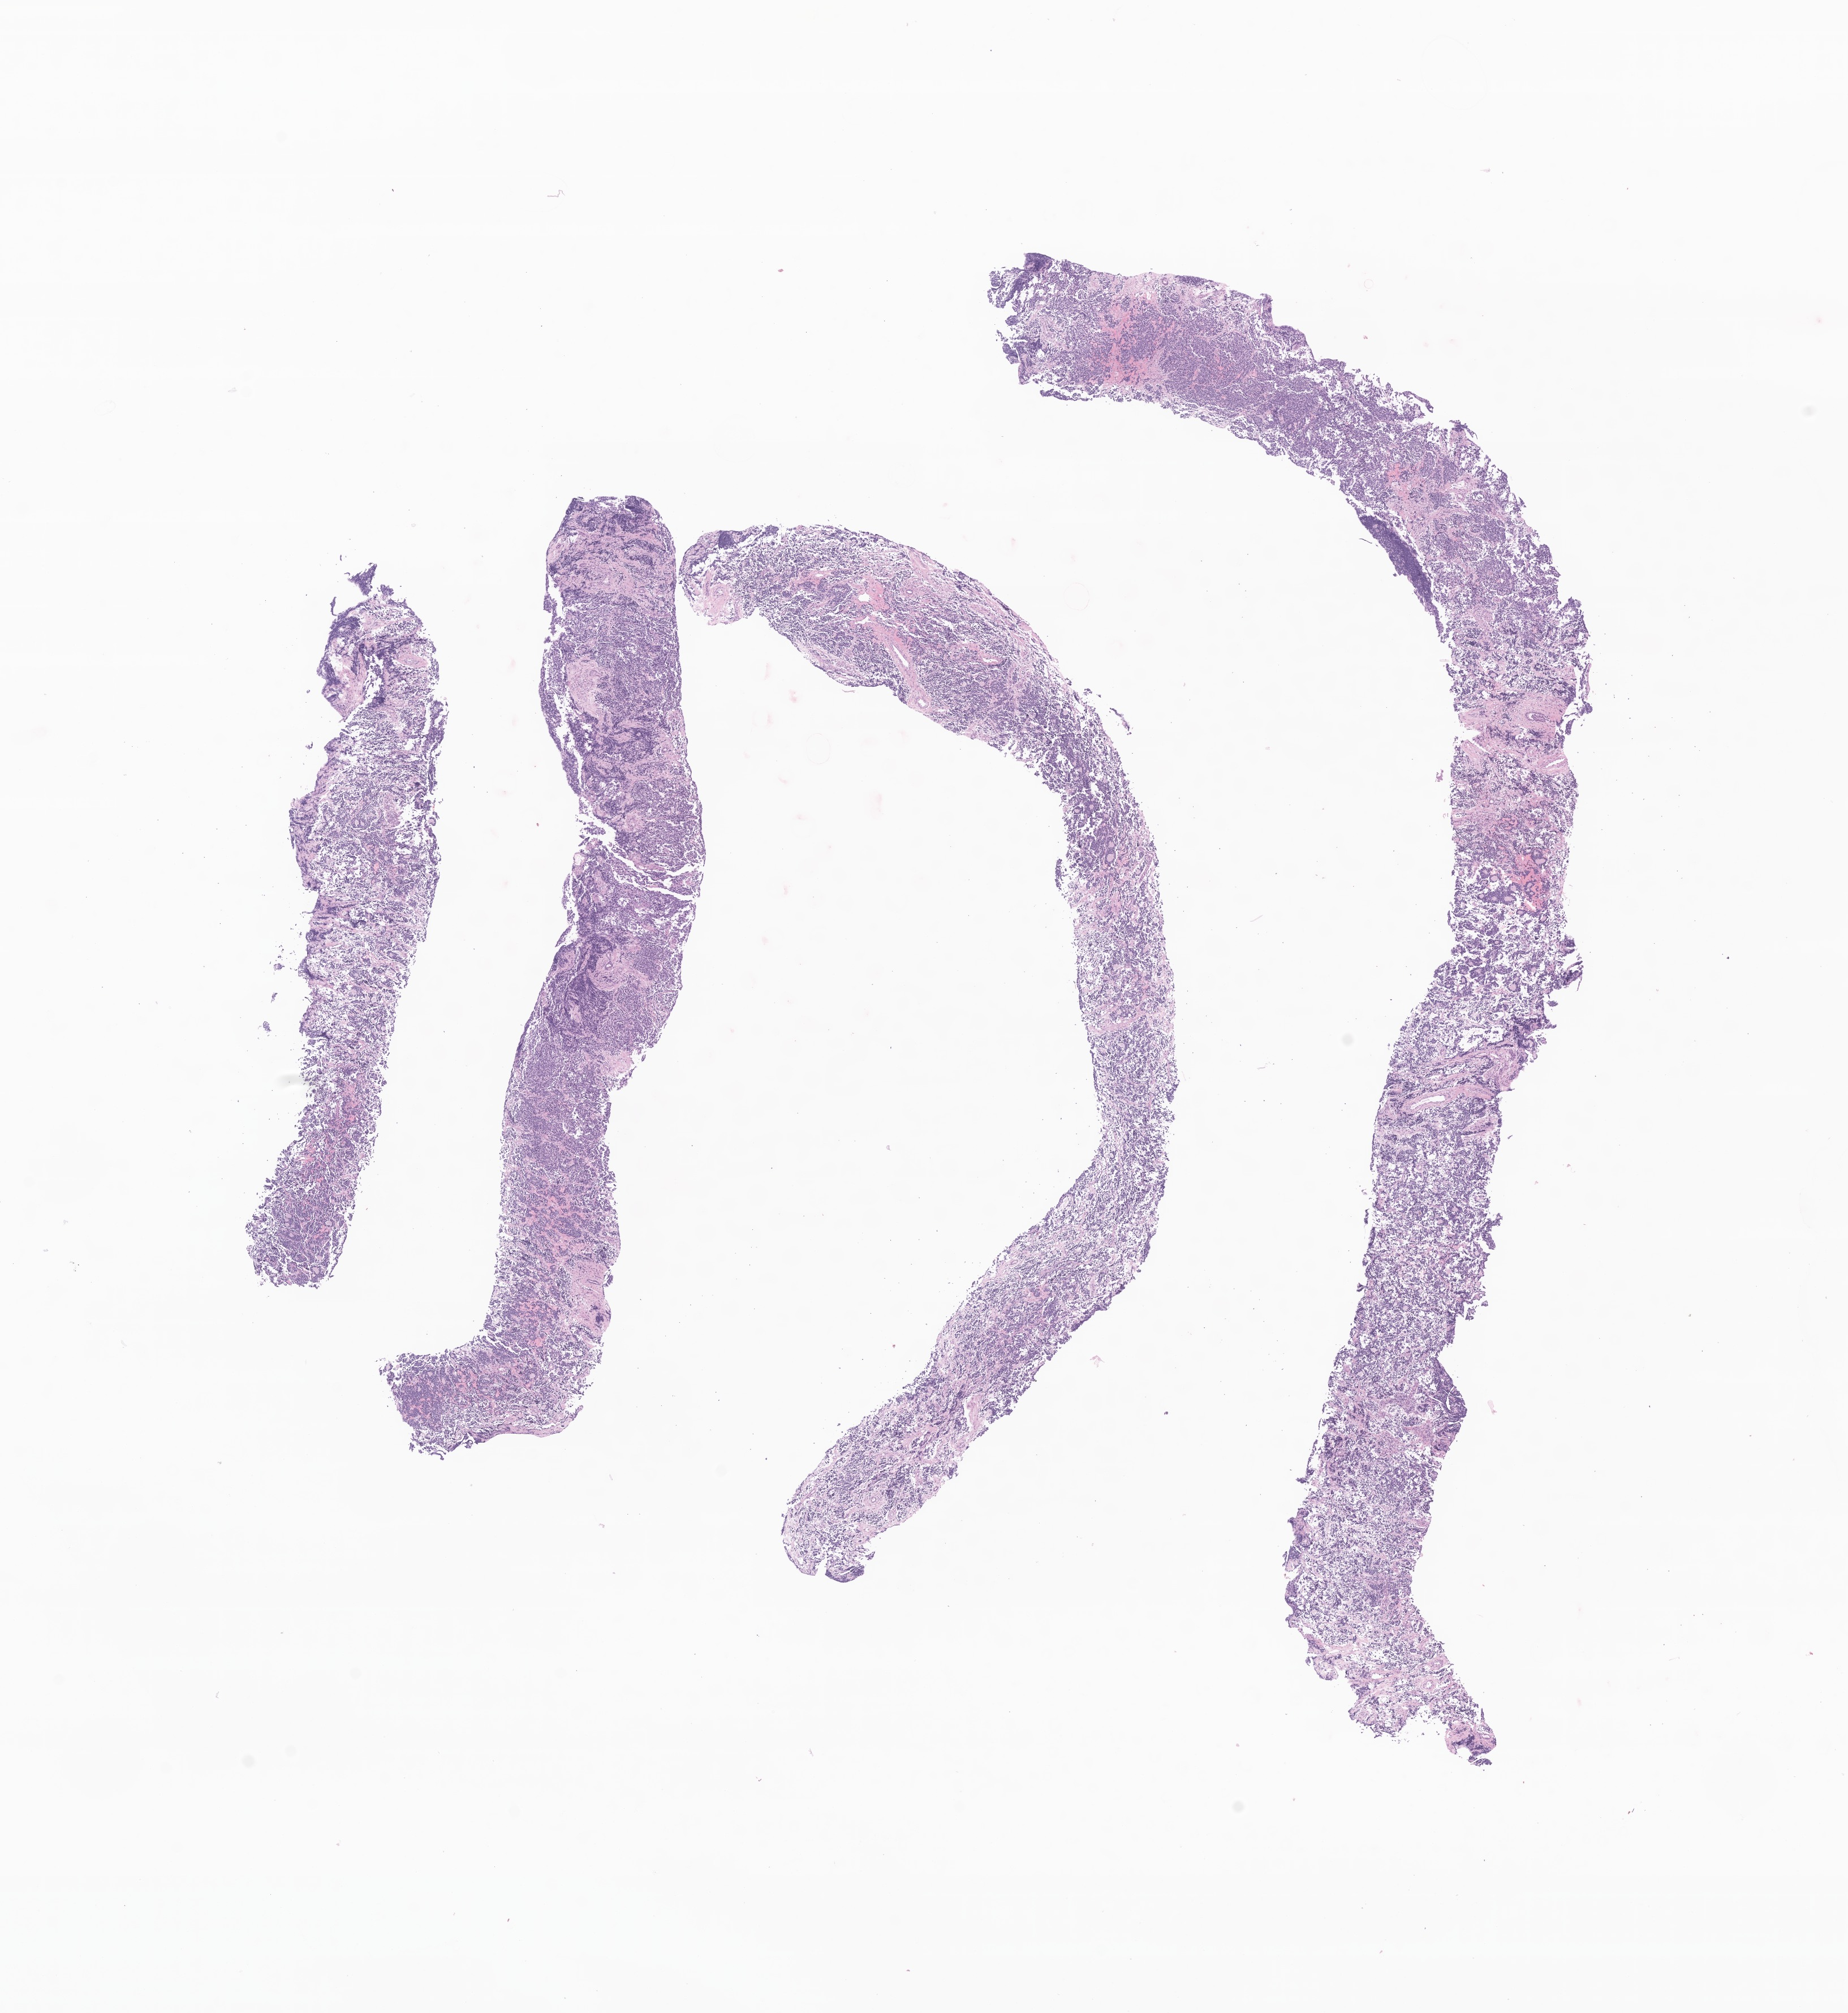
Whole-slide image, haematoxylin and eosin stain of tumor tissue from the adrenal gland, a low-resolution overview of the entire scanned area, about 13.8 x 15.0 mm, formalin-fixed paraffin-embedded section. Female patient, age 2 days.
* recorded diagnosis: Neuroblastoma, NOS